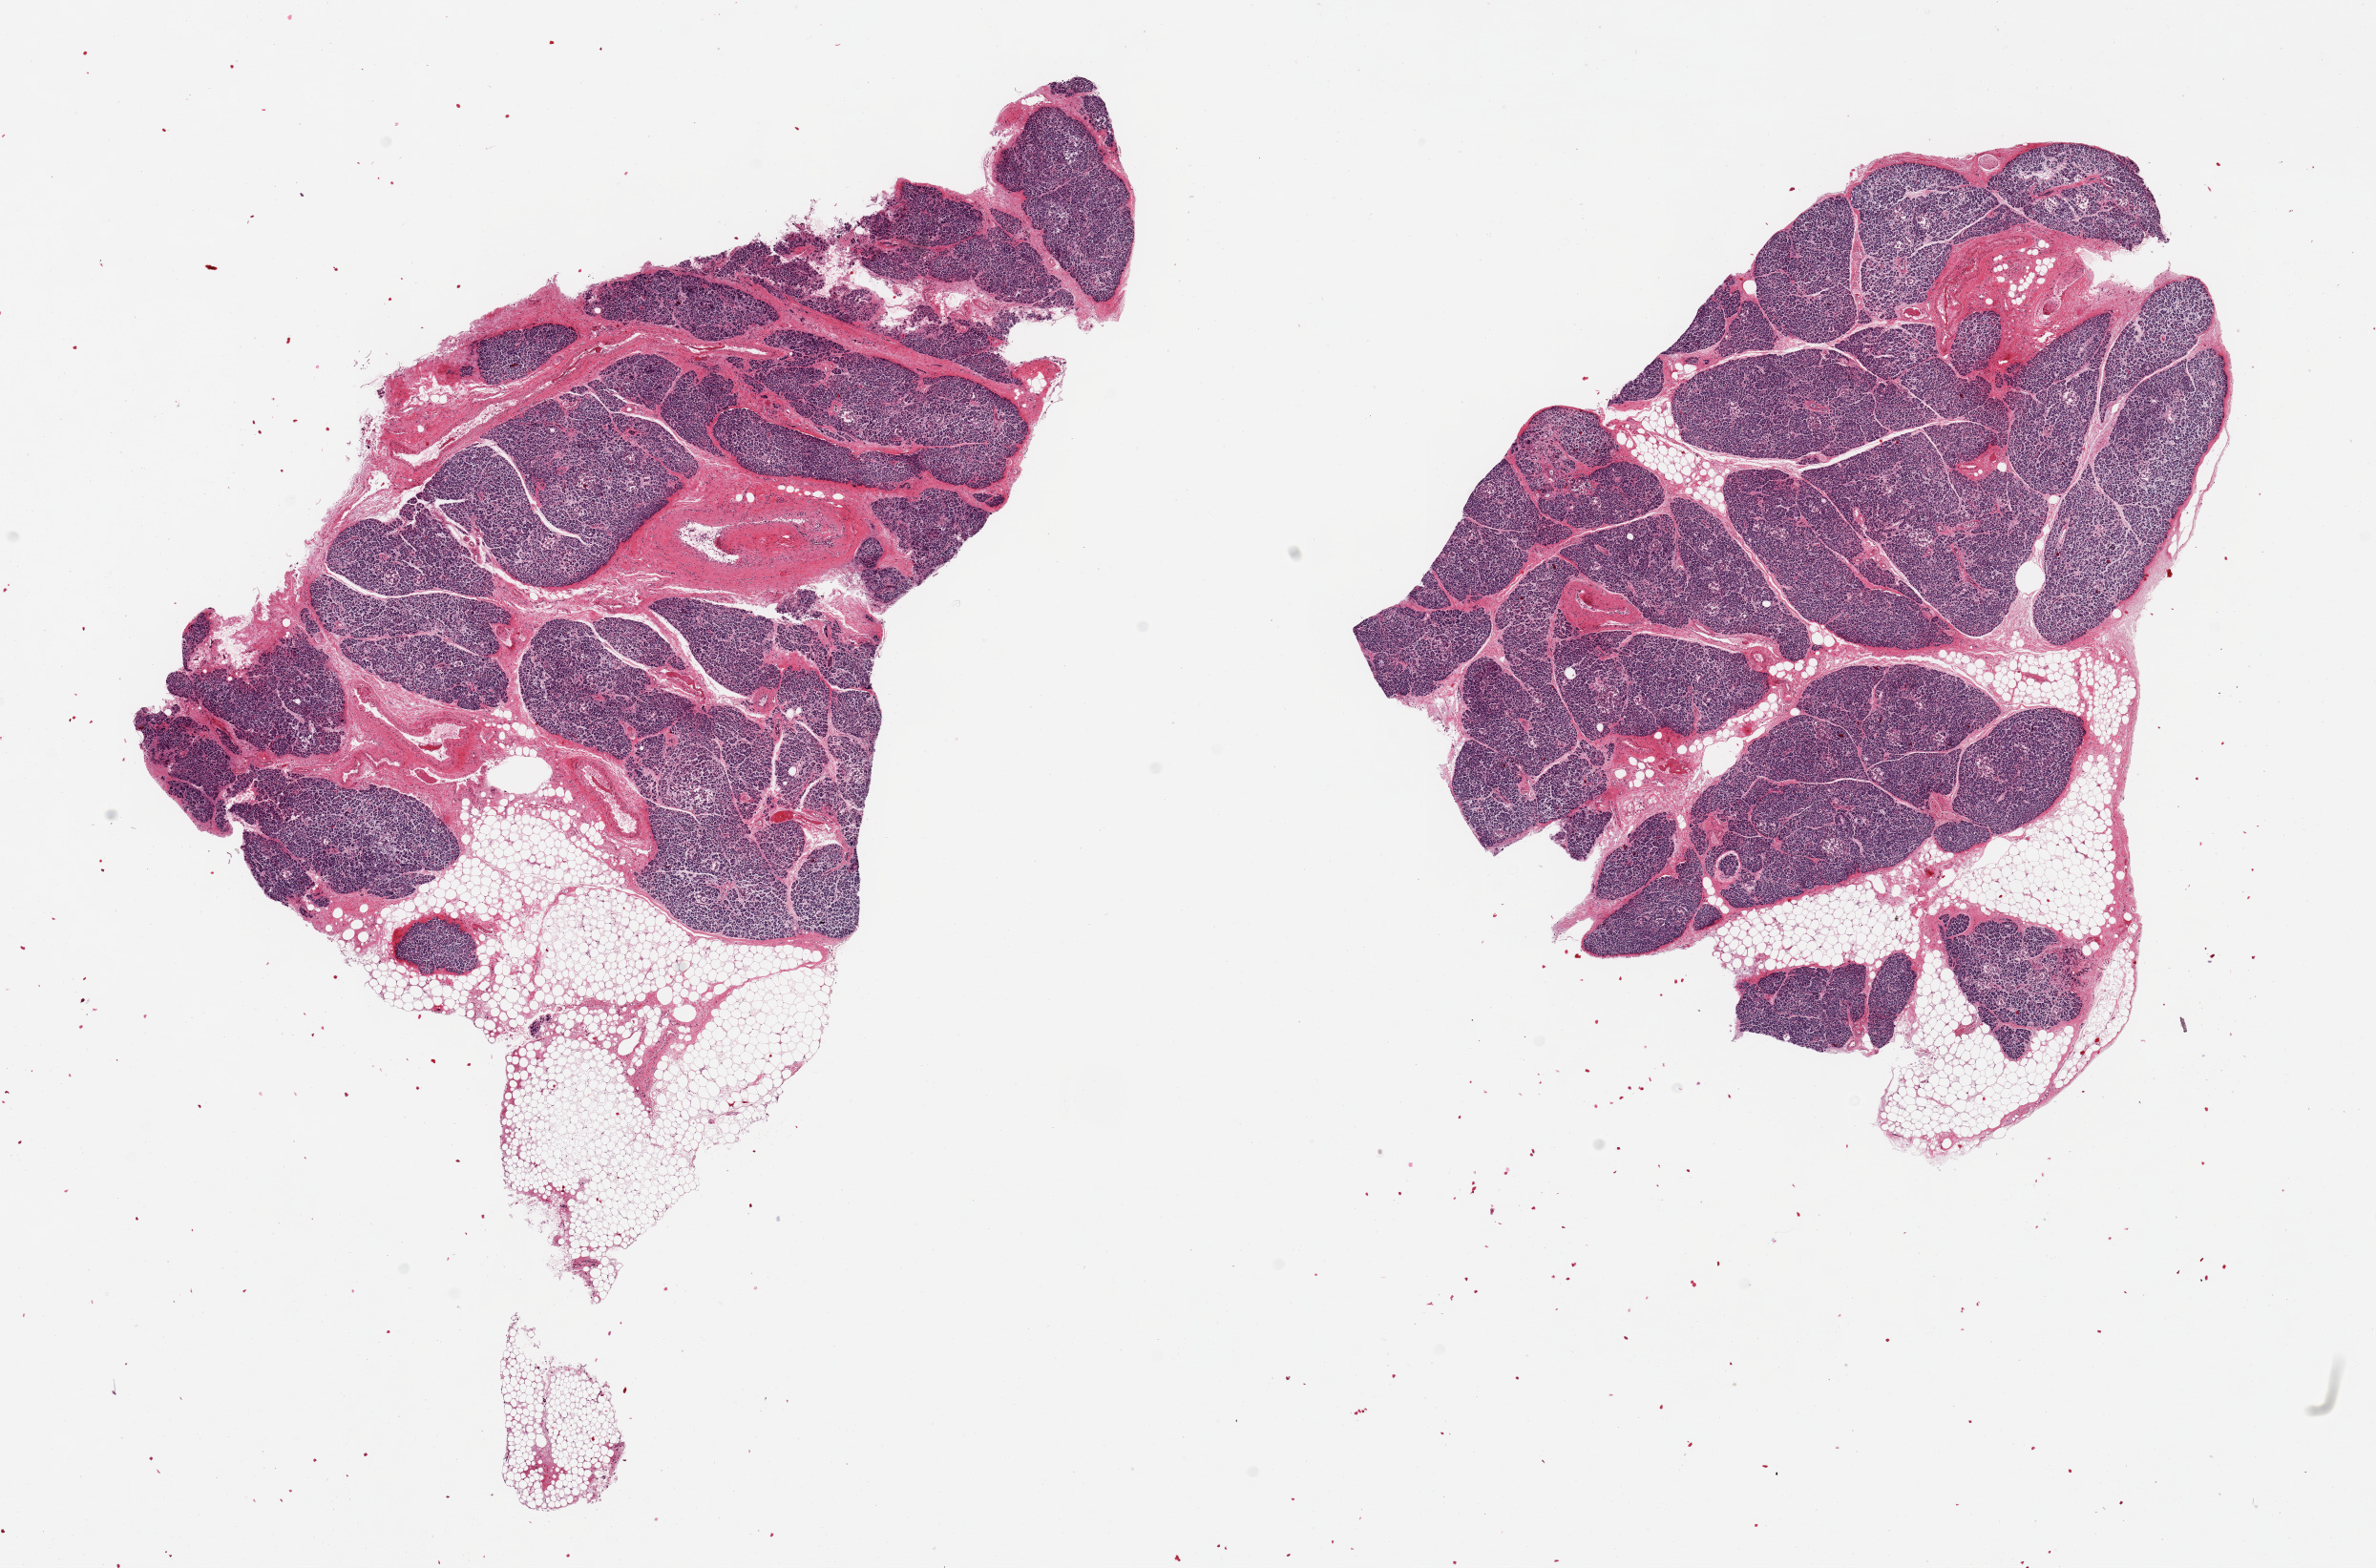
H&E whole-slide image — whole scanned area (about 19.7 x 13.0 mm, slide scanned at 20x) shown as a low-resolution overview. PAXgene-fixed paraffin-embedded (PFPE) section. Target tissue: pancreas. Donor tissue sample. Donor sex: female.
- review note (as recorded): 2 pieces, ~20% fat; Islets degraded, moderate-advanced saponification